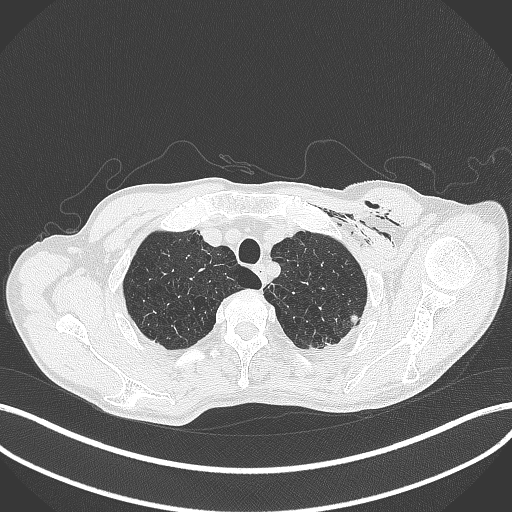
Chest CT, one axial slice. Reconstruction kernel B70f. Lung window (W 1500 / L -600 HU). 1 mm slice thickness. 512 × 512 image matrix, field of view 400 × 400 mm. Male patient, age 58 years. Case-level facts recorded for this patient, not image findings: clinical TNM (as recorded): T3 N0 M0.
Outlined on this slice (rectangle marked by the reading radiologist):
- lung tumour (recorded histology: adenocarcinoma): bounding box [x1, y1, x2, y2] px = [346, 311, 361, 328]